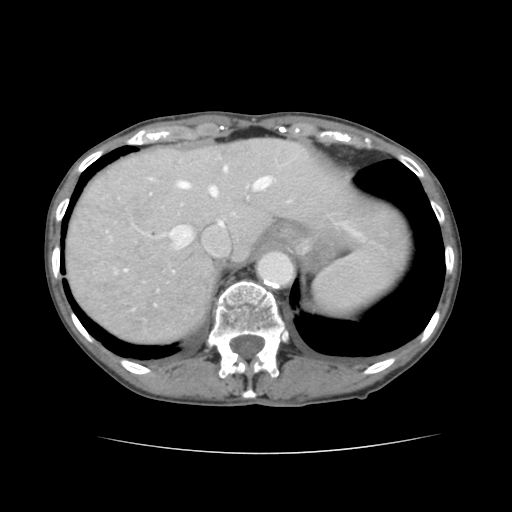
Contrast-enhanced abdominal CT, one axial slice. Slice 114 of 136 in the series (ordered by position). Intravenous contrast given. Soft-tissue window (W 400 / L 40 HU). 2.5 mm slice thickness. 512 × 512 image matrix. Female patient, age 77 years. Case-level facts recorded for this patient, not image findings: diagnosis: colorectal cancer liver metastases, imaged before liver resection; multiple liver metastases: yes; largest metastasis: 3 cm; disease in both lobes: no.
Outlined on this slice (expert manual segmentation):
- hepatic veins: bounding box (x1, y1, x2, y2) in pixels: (131, 167, 271, 256)
- liver: (66, 138, 405, 342)
- planned liver remnant (the part of the liver to remain after resection): (170, 138, 405, 256)